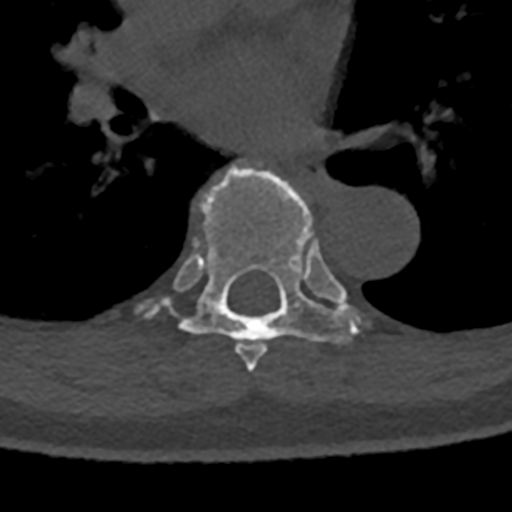
CT including the spine, one axial slice; reconstruction kernel Br40s/3; 120 kVp; bone window (W 1800 / L 400 HU); 0.5 mm slice thickness; 512 × 512 image matrix, field of view 160 × 160 mm. Patient: male, 74 years. Case-level facts recorded for this patient, not image findings: primary cancer: renal; vertebrae with lytic lesions (as recorded): T10, L1, L2, L3, L4, L5.
Annotated regions visible in this slice (semi-automatic segmentation, software-assisted and operator-edited):
- T6 vertebra: box from (x=236, y=342) to (x=267, y=372) px
- T7 vertebra: (x=147, y=165)–(x=362, y=361)